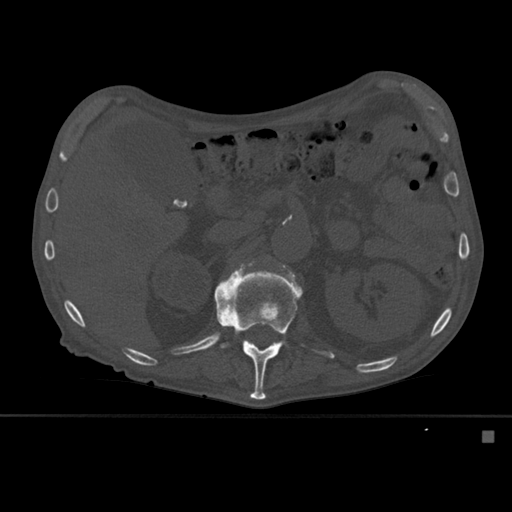
CT including the spine, one axial slice. Slice 254 of 527 in the series (ordered by position). Bone window (W 1800 / L 400 HU). 512 × 512 image matrix, field of view 373 × 373 mm. Patient: male, 78 years. From the clinical record (not read from this slice): primary cancer: prostate.
Outlined on this slice (semi-automatic segmentation, software-assisted and operator-edited):
- L1 vertebra: bounding box (x1, y1, x2, y2) in pixels: (214, 269, 302, 400)